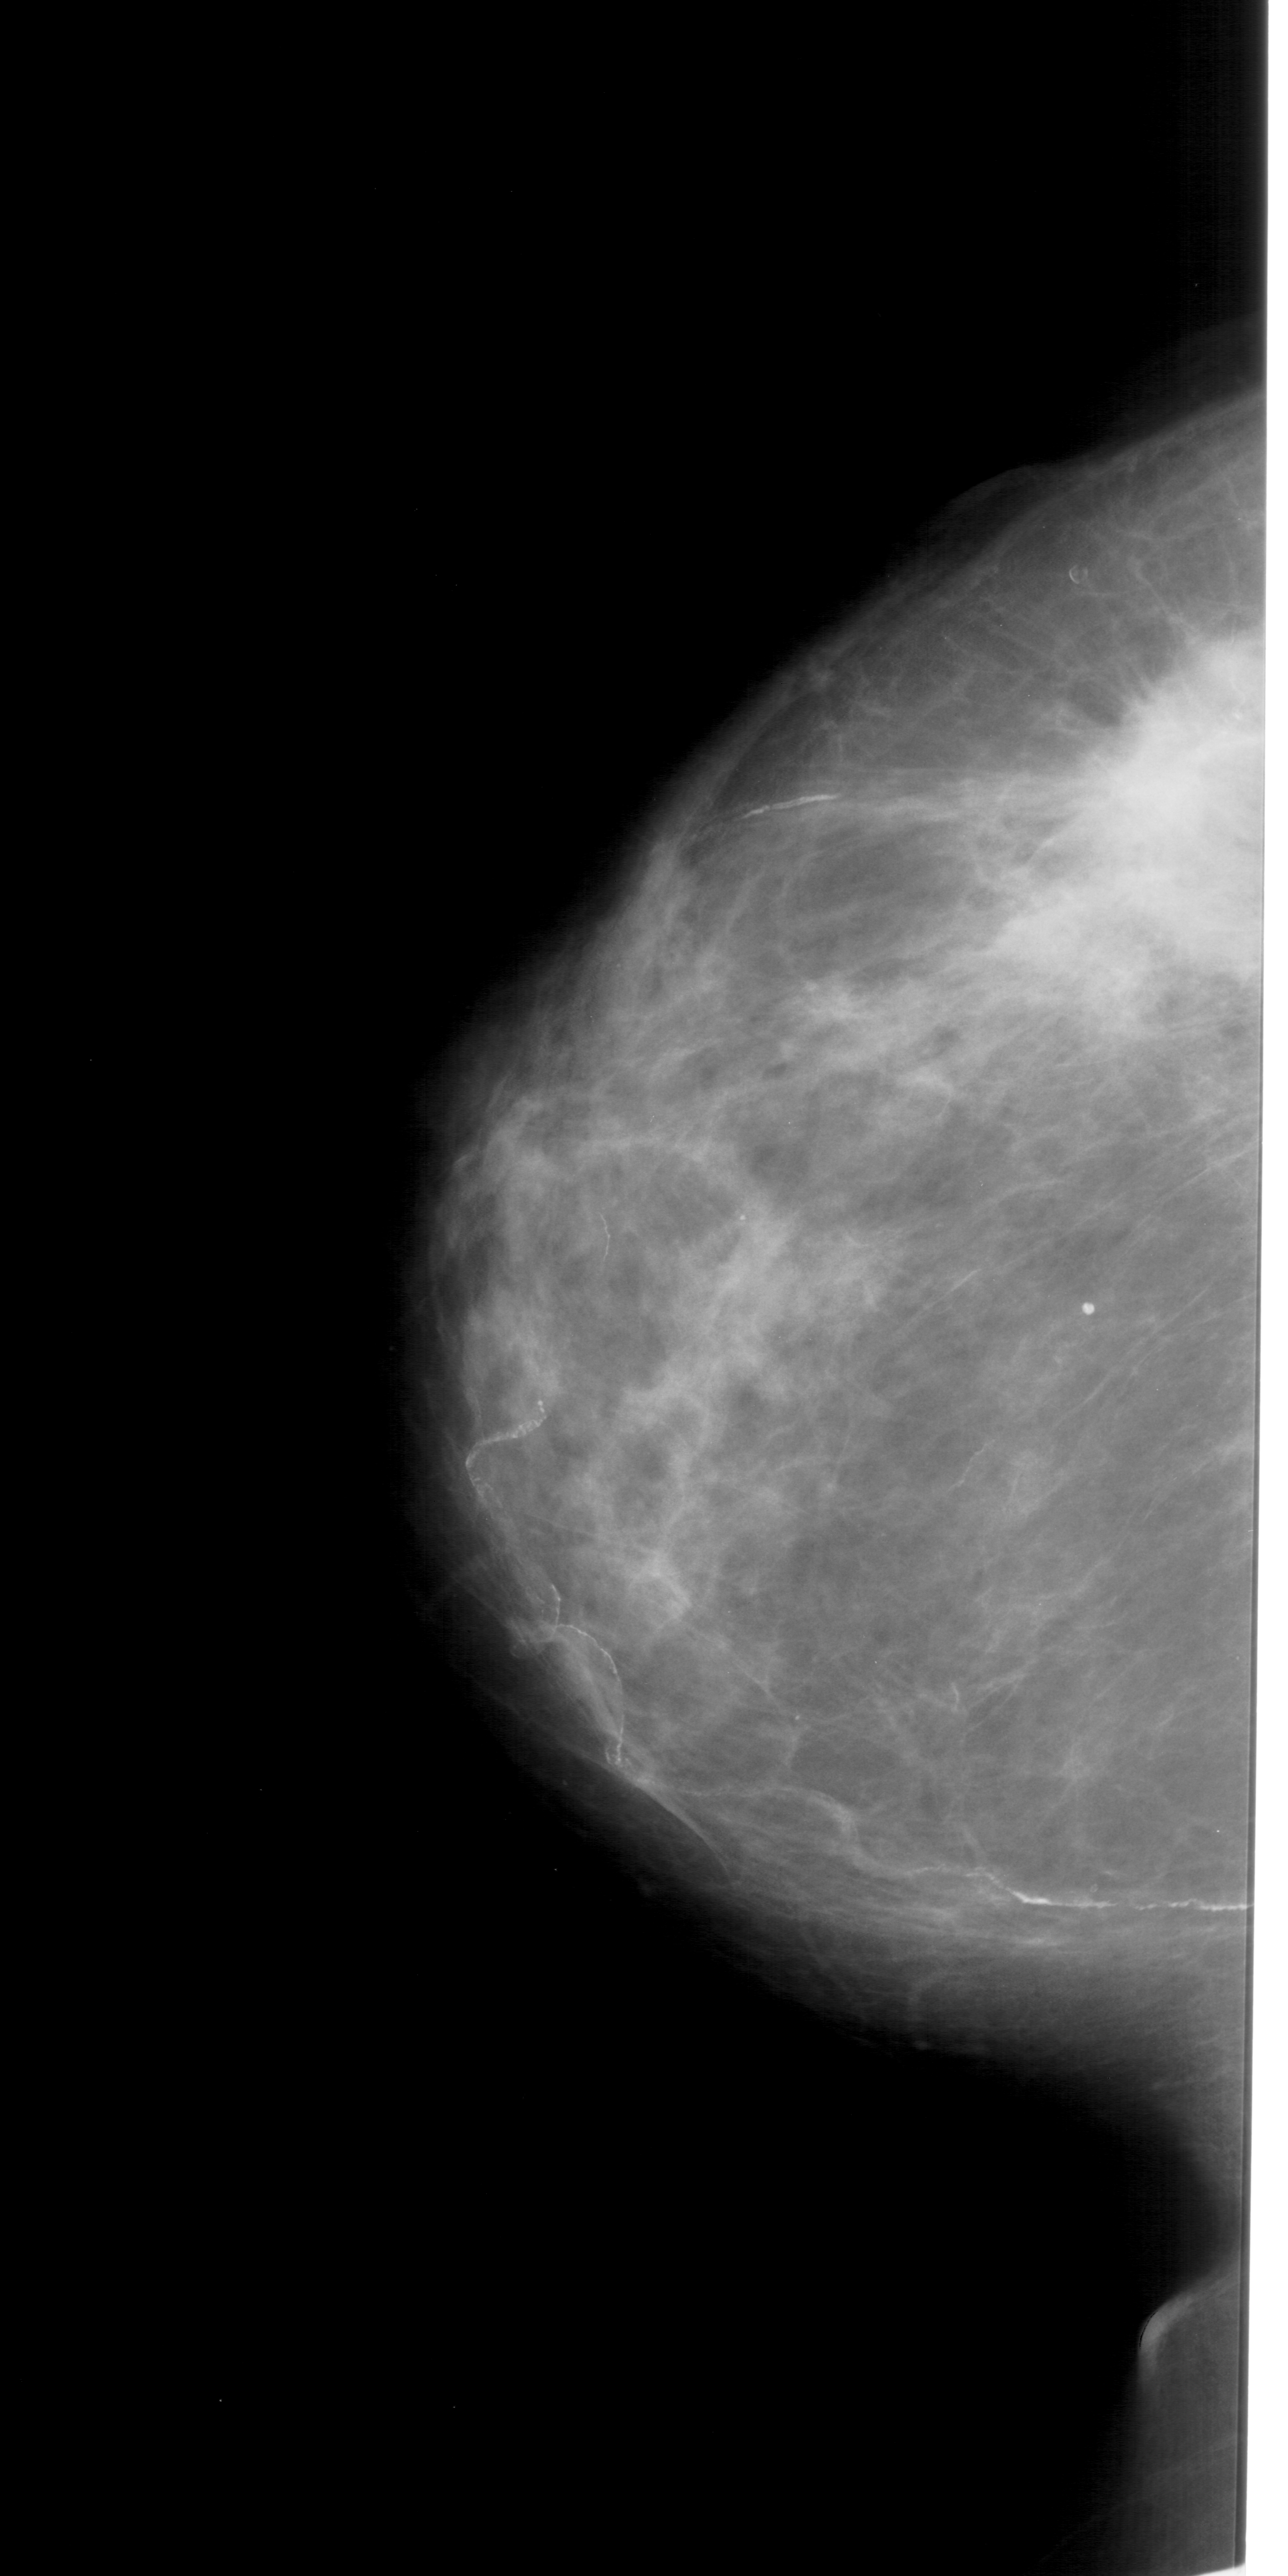
Digitized screen-film mammogram, left breast, CC view, BI-RADS breast density category 3 (scale 1–4).
- Marked findings (only marked abnormalities are described; nothing is implied about the rest of the image): mass, shape irregular, margins spiculated; BI-RADS assessment category 5; pathology (as recorded): malignant.